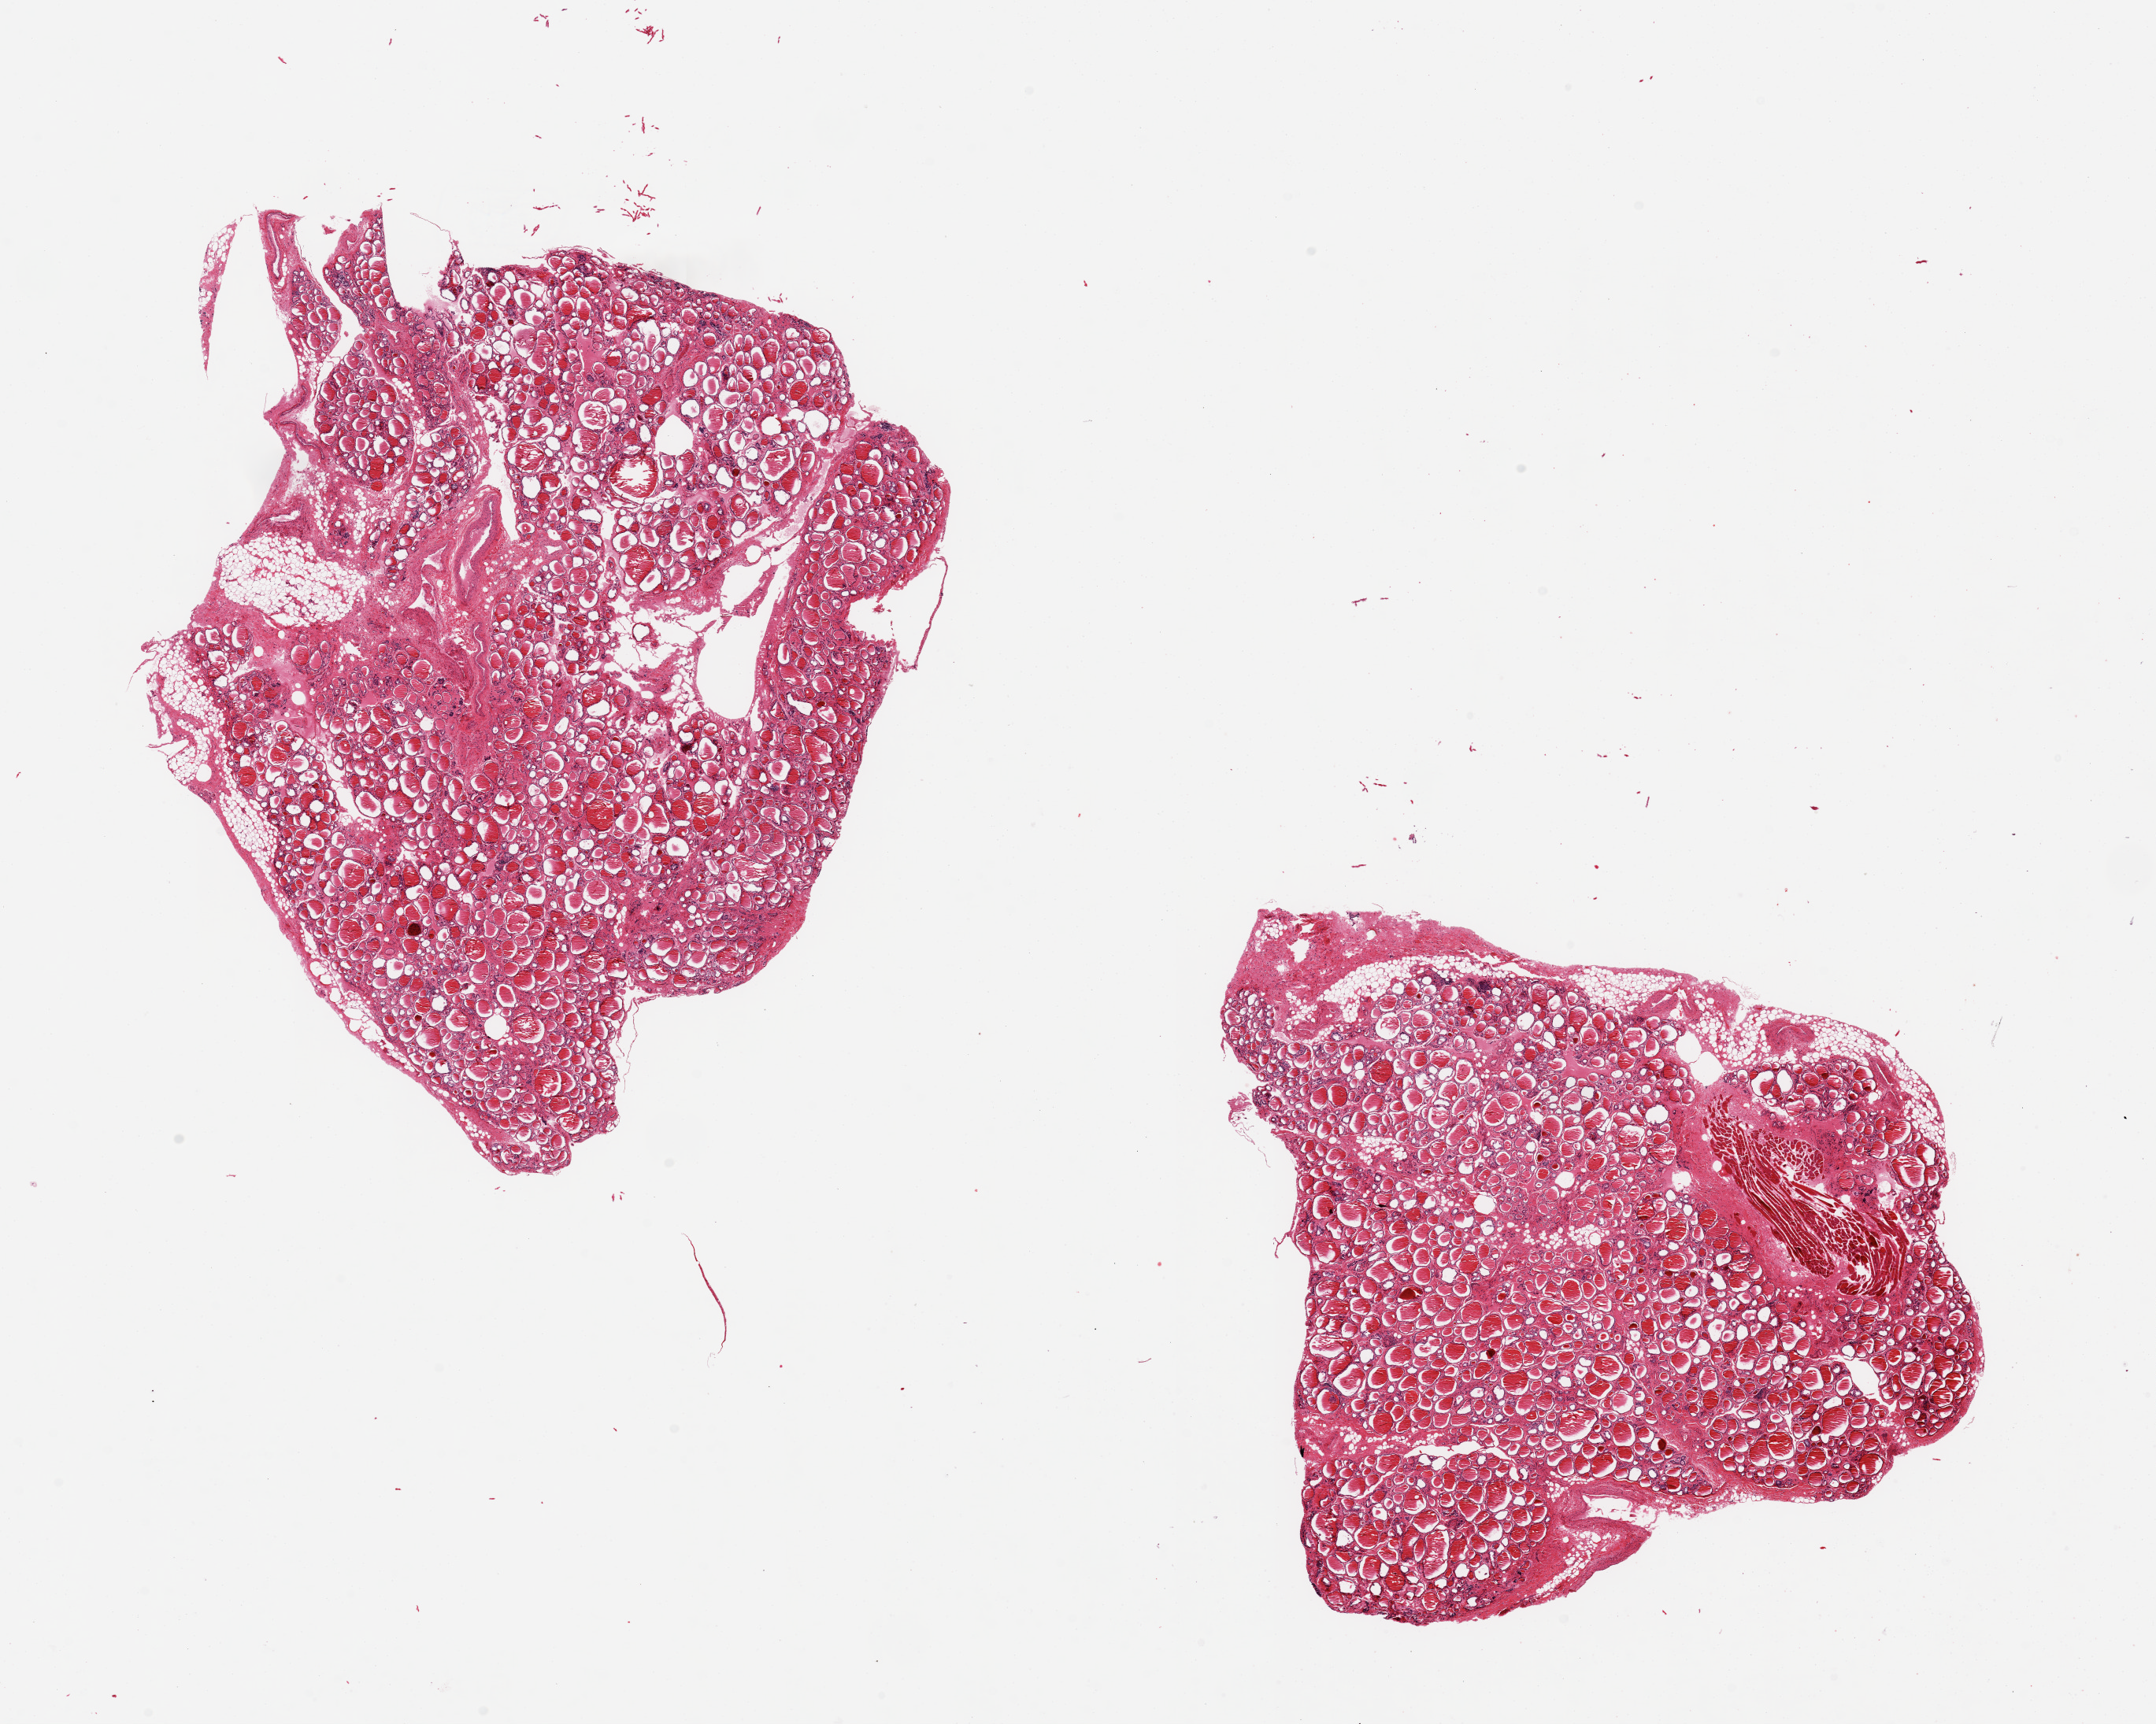
Hematoxylin and eosin (H&E) whole-slide image — whole scanned area (about 21.7 x 17.3 mm) shown as a low-resolution overview. PAXgene-fixed paraffin-embedded (PFPE) section. Sampled site (target tissue): thyroid. Donor tissue sample. Donor: male.
Pathologist's review note for this sample: 2 pieces ~8x7mm, focus of entrapped skeletal muscle (probable embedding artifact).